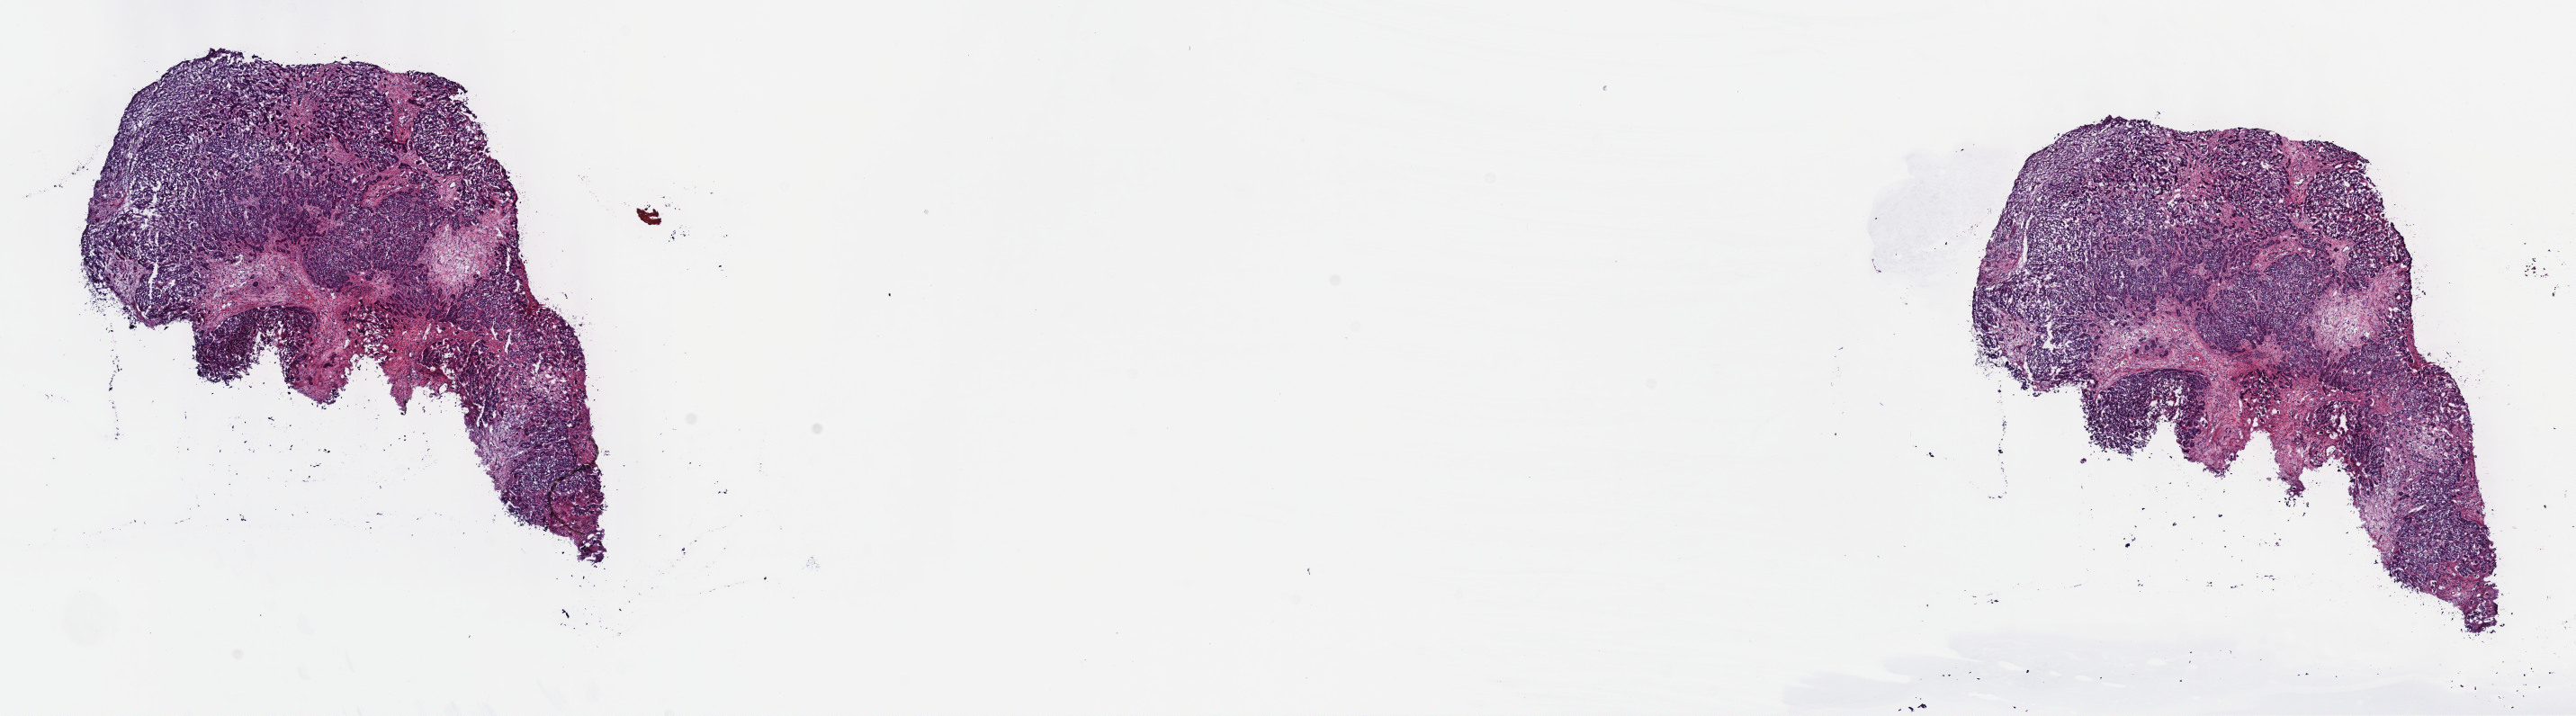
Digitized Hematoxylin and eosin (H&E) stained tissue section (whole slide) — low-resolution overview of the scanned area, about 23.2 x 6.4 mm; frozen section from the top of the tissue portion; primary tumour sample from the bile duct. Male, age 58 years at initial diagnosis.
Histologic diagnosis: Cholangiocarcinoma (intrahepatic bile duct).